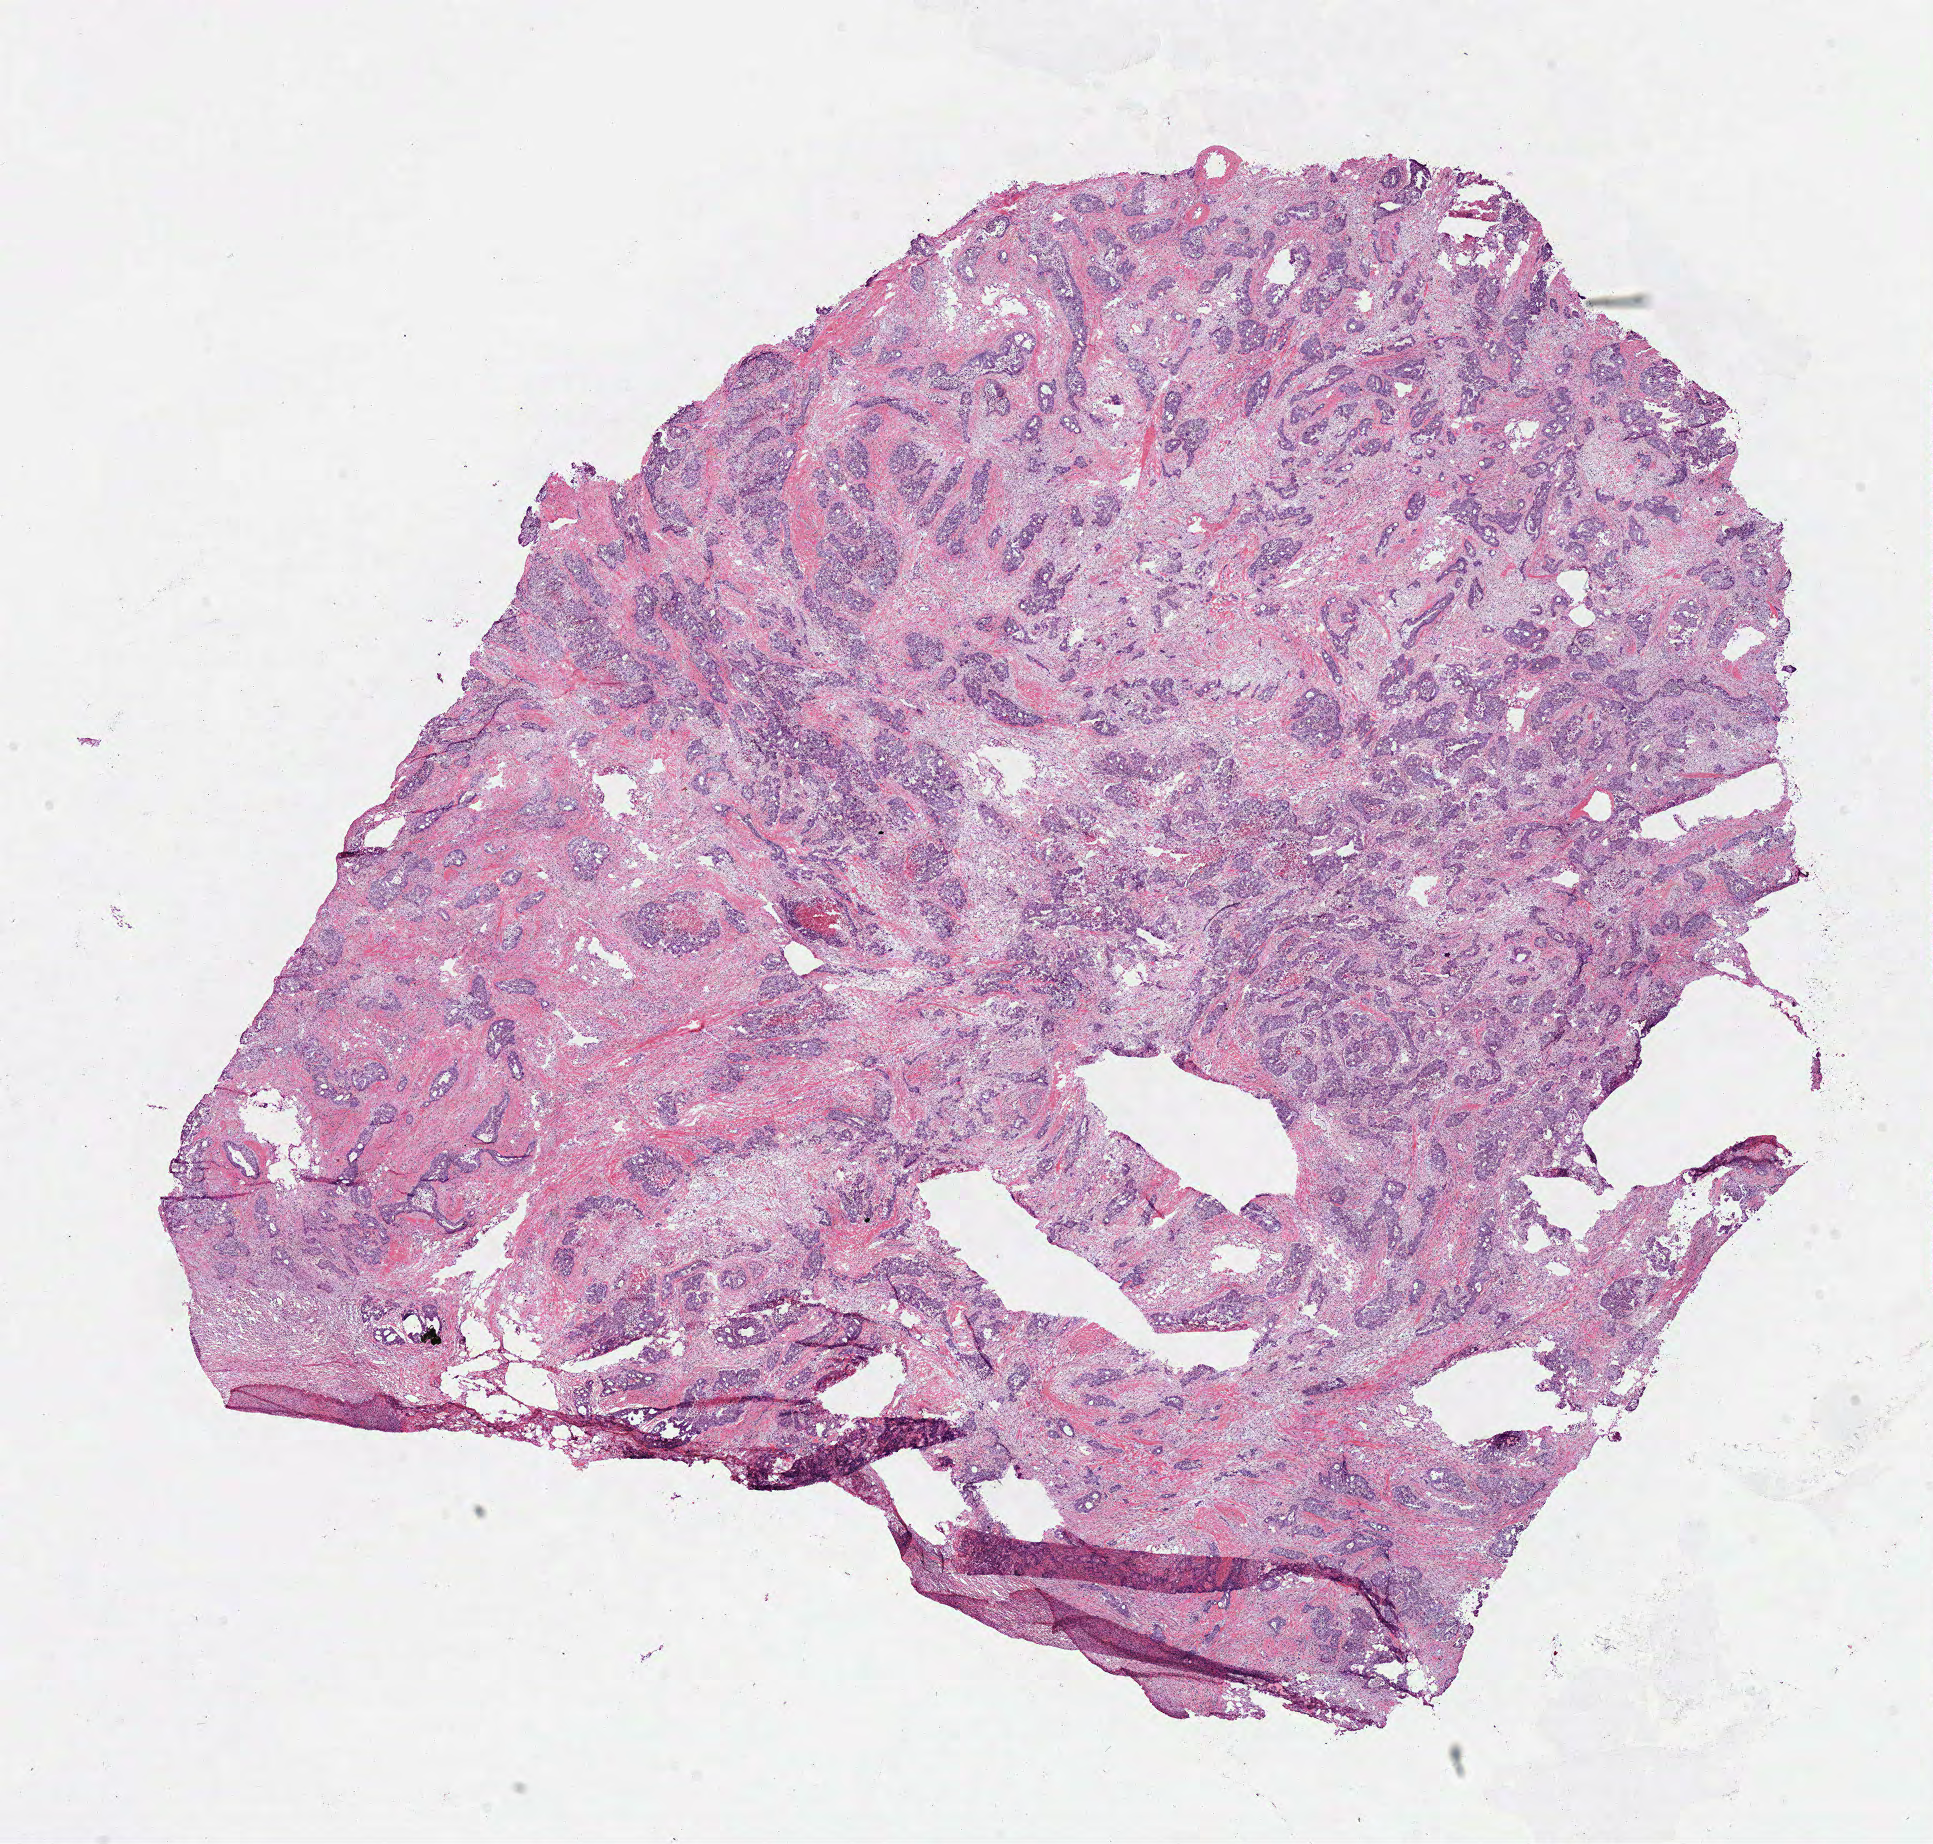
Whole-slide histology image, Hematoxylin and eosin (H&E) stained, low-resolution overview of the scanned area, about 15.2 x 14.5 mm (acquisition: 40x scan); frozen section; sample: primary tumour, rectum. Patient: male, age at initial diagnosis 62 years. Composition of this section per pathologist review: tumour cells 70%, tumour nuclei 70%, normal cells 0%, stromal cells 25%, necrosis 5%.
AJCC pathologic stage: IVA (7th edition). Pathologic diagnosis: Adenocarcinoma, NOS (rectosigmoid junction).